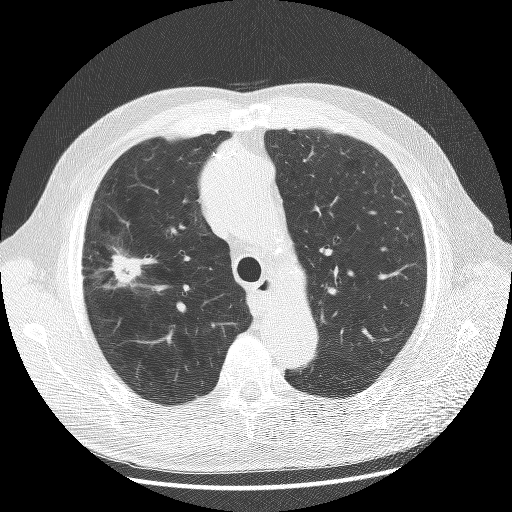
Low-dose screening chest CT, axial slice; baseline annual screen; lung window (W 1500 / L -600 HU); 2.5 mm slice thickness; 120 kVp; slice 43 of 175 in the series; 512 × 512 image matrix. Male participant, aged 70 years at enrolment. Current smoker at enrolment.
Expert-annotated lung lesion, bounding box (x1, y1, x2, y2) in pixels: (76, 236, 148, 306). The screening reader recorded 2 non-calcified nodules or masses ≥4 mm on this exam (left upper lobe, right upper lobe); which of them this box marks is not recorded. Official screen result: positive, change unspecified: nodule(s) >= 4 mm or enlarging nodule(s), mass(es), or other non-specific abnormalities suspicious for lung cancer. Later outcome: lung cancer diagnosed 23 days after this screen — non-small cell carcinoma, right upper lobe, poorly differentiated (G3), stage IA (AJCC 6th edition), 20 mm at pathology.